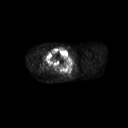
FDG PET of an extremity soft-tissue mass (from a PET/CT study), one axial slice; slice 261 of 311 in the series (ordered by position); 3.27 mm slice thickness; 128 × 128 image matrix, field of view 700 × 700 mm. Male patient, age 50 years. From the clinical record (not read from this slice): histological type: undifferentiated - pleiomorphic; grade: high; site of the primary tumour: right thigh.
Outlined on this slice (expert contour drawn on MRI and transferred to this co-registered scan by the dataset authors):
- gross tumour volume including surrounding oedema: bounding box (x1, y1, x2, y2) in pixels: (43, 47, 66, 68)
- gross tumour volume (mass): (45, 48, 66, 68)